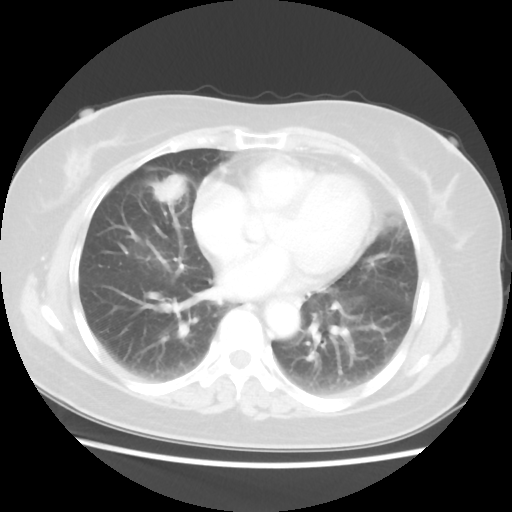
Chest CT, one axial slice. Slice 21 of 48 in the series (ordered by position). Reconstruction kernel STANDARD. 100 kVp. Lung window (W 1500 / L -600 HU). 5 mm slice thickness. 512 × 512 image matrix, field of view 343 × 343 mm. Female patient, age 61 years. Case-level facts recorded for this patient, not image findings: clinical TNM (as recorded): T1c N0 M0.
Annotated regions visible in this slice (bounding box drawn by a radiologist):
- lung tumour (recorded histology: adenocarcinoma): bounding box (x1, y1, x2, y2) in pixels: (152, 174, 184, 209)